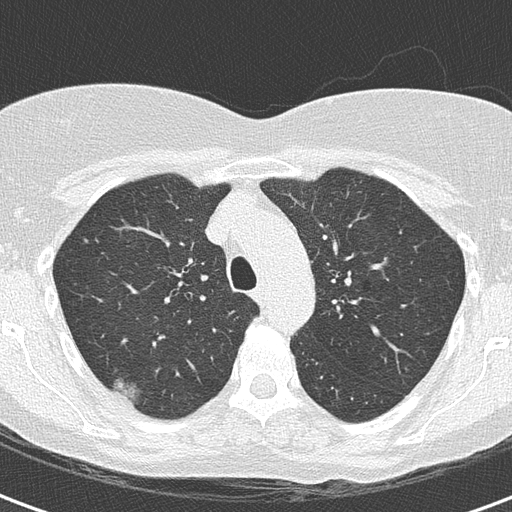
Axial slice from a low-dose chest CT screening exam; second annual screen; lung window (W 1500 / L -600 HU); 2 mm slice thickness; lung (sharp) reconstruction kernel (B50f); 120 kVp. Female participant, aged 56 years at enrolment.
Lesion marked by an expert reader, bounding box <94,365,152,414> (left, top, right, bottom; pixels). Reader record for this screening exam (exam-level; its link to the box is not recorded): non-calcified nodule or mass ≥4 mm, right upper lobe, 18 × 18 mm, mixed attenuation, pre-existing on the prior screen: yes. Lung cancer was diagnosed 93 days after this screen: bronchiolo-alveolar adenocarcinoma, NOS, right upper lobe, well differentiated (G1), stage IA (AJCC 6th edition), 15 mm at pathology.